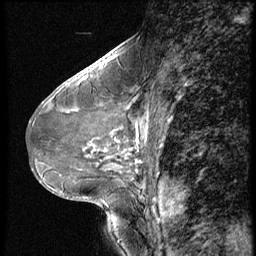
Breast MRI (dynamic contrast-enhanced), one sagittal slice; position 27 of 56 along the scan axis; dynamic contrast-enhanced series, image 2 of 3 at this slice position (ordered by acquisition); 1.5 T; TE 4.2 ms, TR 9 ms; 2.5 mm slice thickness; 256 × 256 image matrix, field of view 180 × 180 mm. Female patient, age 46 years. Case-level facts recorded for this patient, not image findings: setting: breast cancer imaged before/during neoadjuvant chemotherapy; receptor status: HER2-positive.
Structures marked on this image (semi-automatically segmented with operator editing):
- analysis volume of interest (the breast-tissue region the enhancement analysis was run in; not a lesion): box from (x=64, y=98) to (x=174, y=182) px
- tumour enhancement mask (voxels above the 140 % enhancement threshold inside the analysis volume of interest): (x=116, y=137)–(x=140, y=164)